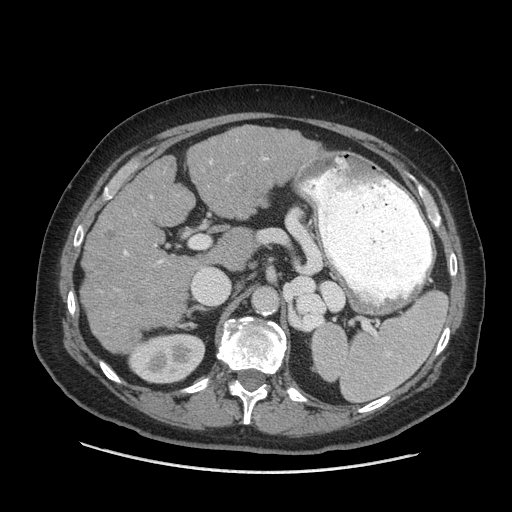
Contrast-enhanced abdominal CT (liver protocol), one axial slice. Position 35 of 77 along the scan axis. Reconstruction kernel STANDARD. Soft-tissue window (W 400 / L 40 HU). 2.5 mm slice thickness. 512 × 512 image matrix, field of view 420 × 420 mm. From the clinical record (not read from this slice): diagnosis: hepatocellular carcinoma (patient treated with transarterial chemoembolisation; whether this scan precedes or follows treatment is not stated here); TNM stage (as recorded): Stage-I; Child-Pugh class: A; tumour differentiation: well differentiated; tumour nodularity: uninodular.
Structures marked on this image (semi-automatically segmented with operator editing):
- liver parenchyma outside the tumour (the mass and vessels are separate outlines, so this box may not span the whole liver): bounding box [x1, y1, x2, y2] px = [80, 126, 326, 352]
- liver vessels: [124, 157, 267, 264]